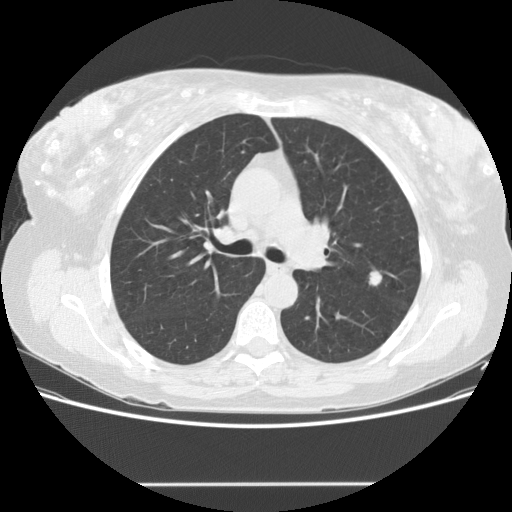
Chest CT (low-dose screening protocol), one axial image; second annual screen; lung window (W 1500 / L -600 HU); standard (soft-tissue) reconstruction kernel (STANDARD); slice 54 of 151 in the series. Female participant, aged 57 years at enrolment.
- Expert-annotated lung lesion, box from (x=358, y=264) to (x=391, y=294) px.
- Screening reader's record for this exam (one nodule recorded; not confirmed to be the boxed lesion): non-calcified nodule or mass ≥4 mm, lingula, 10 × 8 mm, smooth margins, soft tissue attenuation, pre-existing on the prior screen: no.
- Official screen result: positive, other.
- Participant outcome: lung cancer diagnosed 125 days after this screen — large cell neuroendocrine carcinoma, left upper lobe, poorly differentiated (G3), stage IB (AJCC 6th edition), 10 mm at pathology.